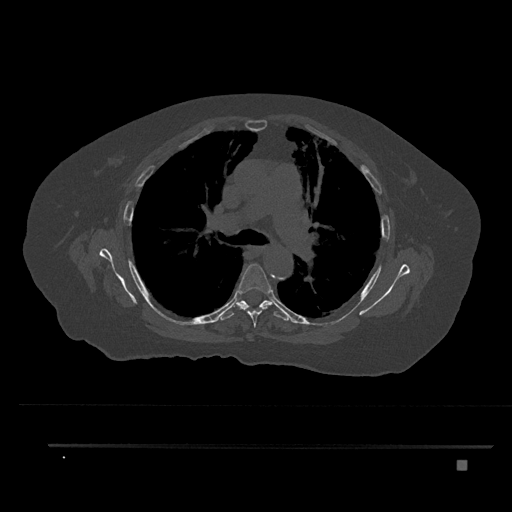
CT including the spine, one axial slice; position 552 of 797 along the scan axis; reconstruction kernel Br40s/3; bone window (W 1800 / L 400 HU); 0.5 mm slice thickness; 512 × 512 image matrix, field of view 437 × 437 mm. Female patient, age 76 years. From the clinical record (not read from this slice): primary cancer: lung.
Annotated regions visible in this slice (semi-automatic segmentation, software-assisted and operator-edited):
- T5 vertebra: bounding box [x1, y1, x2, y2] px = [234, 263, 271, 327]
- T6 vertebra: [219, 300, 290, 321]